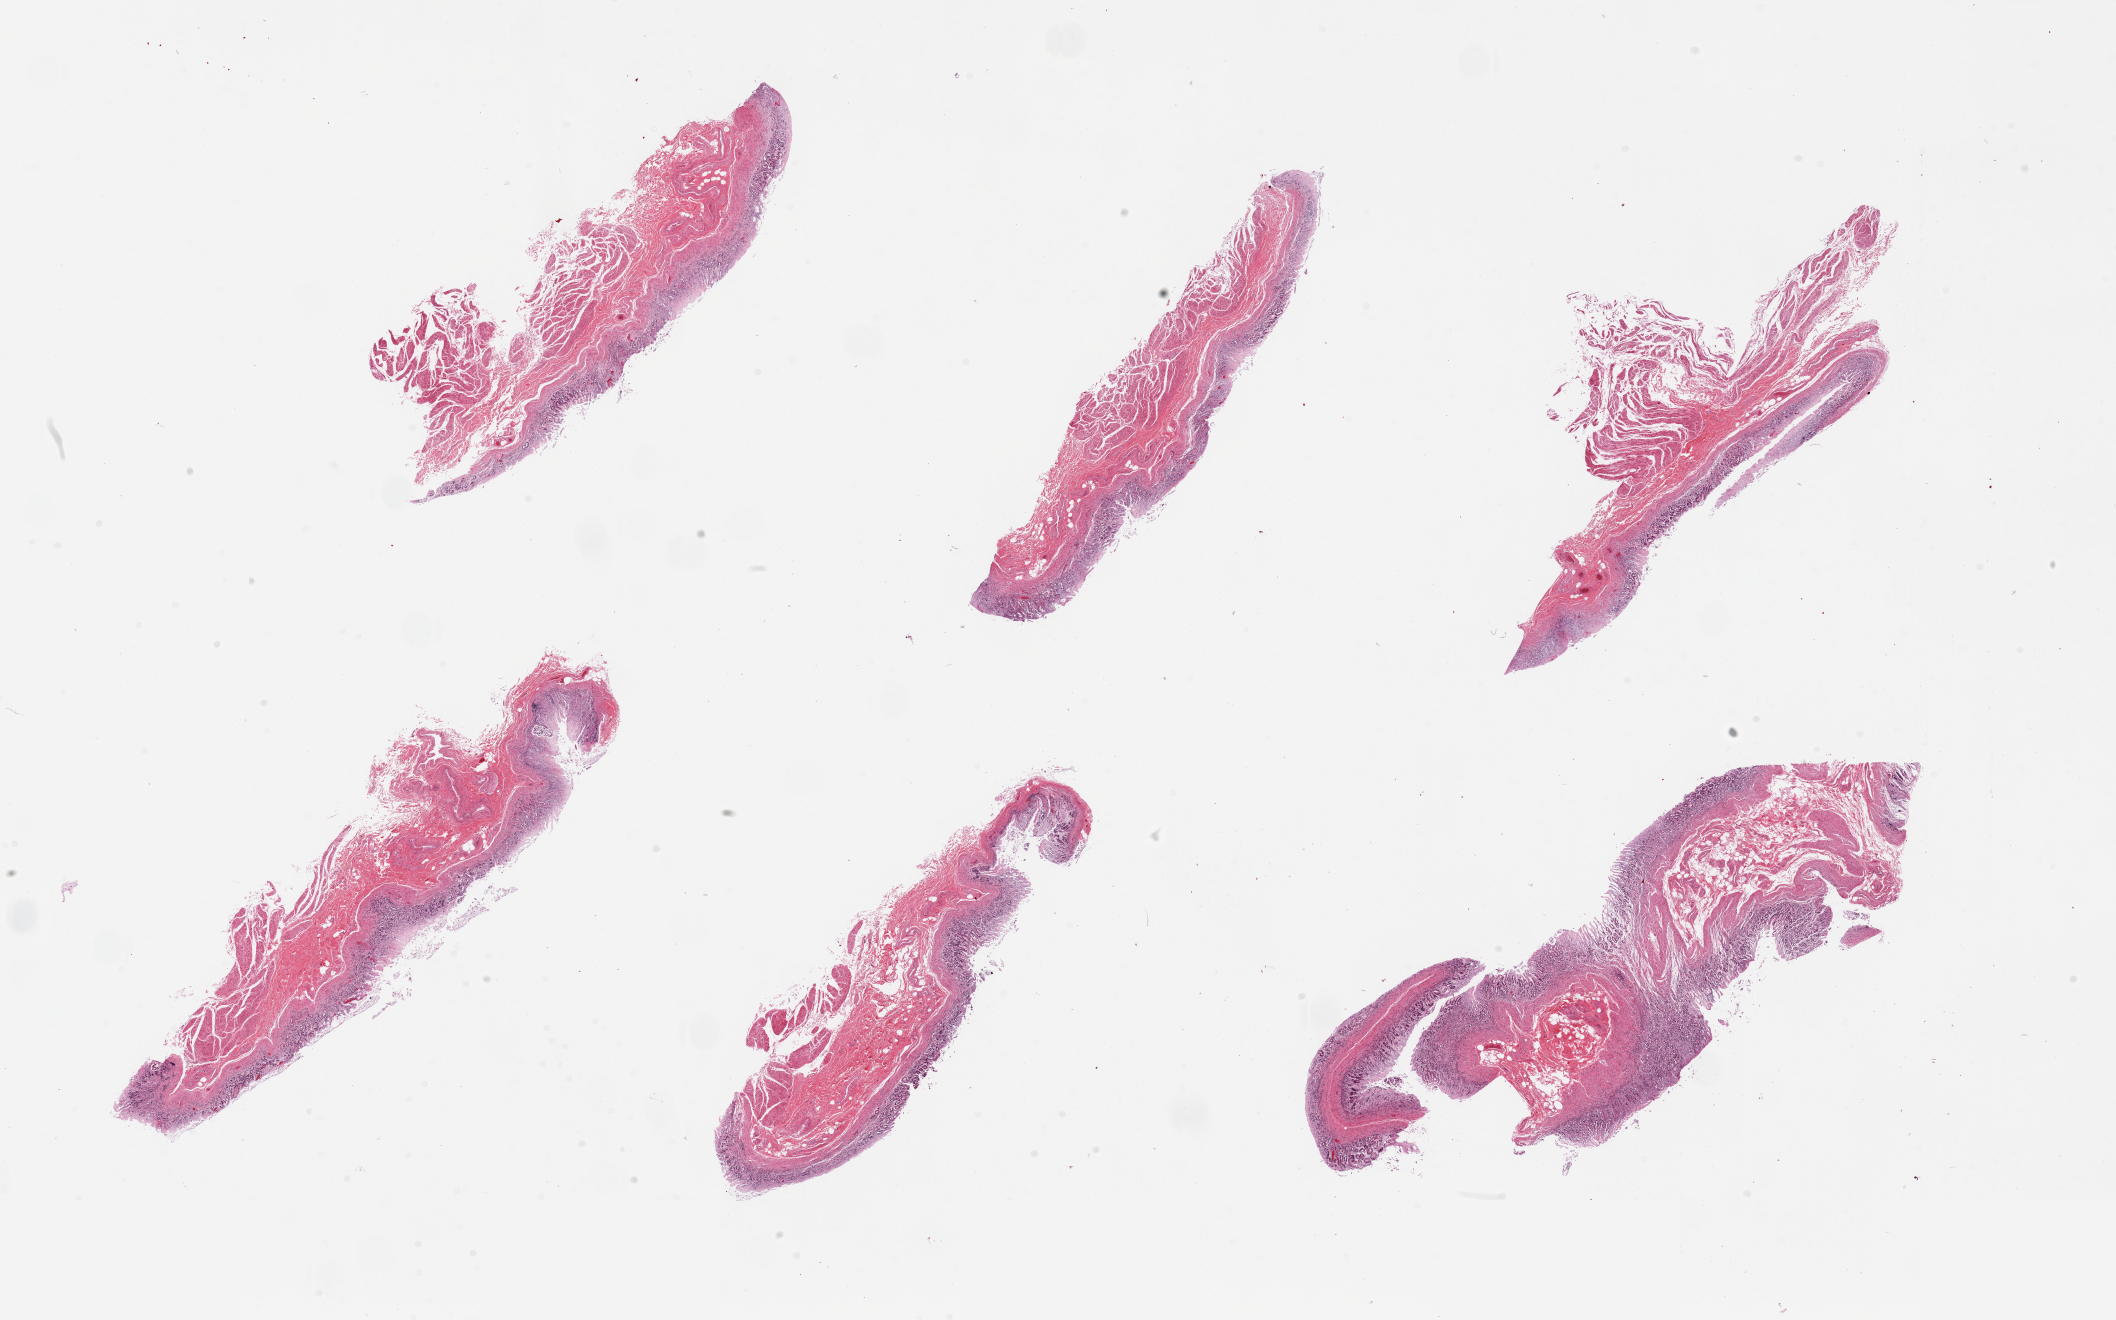
H&E whole-slide image, brightfield, whole scanned area (about 33.5 x 20.9 mm, slide scanned at 20x) shown as a low-resolution overview, PAXgene-fixed paraffin-embedded (PFPE) section, target tissue: stomach, donor tissue sample.
Pathologist's review note for this sample: 6 pieces, mucosa up to ~0.7mm thick but badly autolyzed.